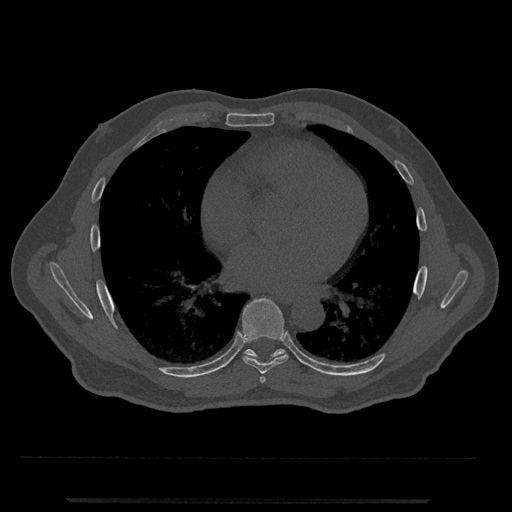
CT including the spine, one axial slice; slice 667 of 797 in the series (ordered by position); 120 kVp; bone window (W 1800 / L 400 HU); 0.5 mm slice thickness; 512 × 512 image matrix, field of view 419 × 419 mm. Patient: male, 63 years. Case-level facts recorded for this patient, not image findings: primary cancer: prostate.
Outlined on this slice (semi-automatic segmentation, software-assisted and operator-edited):
- T6 vertebra: box from (x=260, y=376) to (x=266, y=383) px
- T7 vertebra: (x=241, y=298)–(x=288, y=374)
- T8 vertebra: (x=244, y=348)–(x=286, y=358)